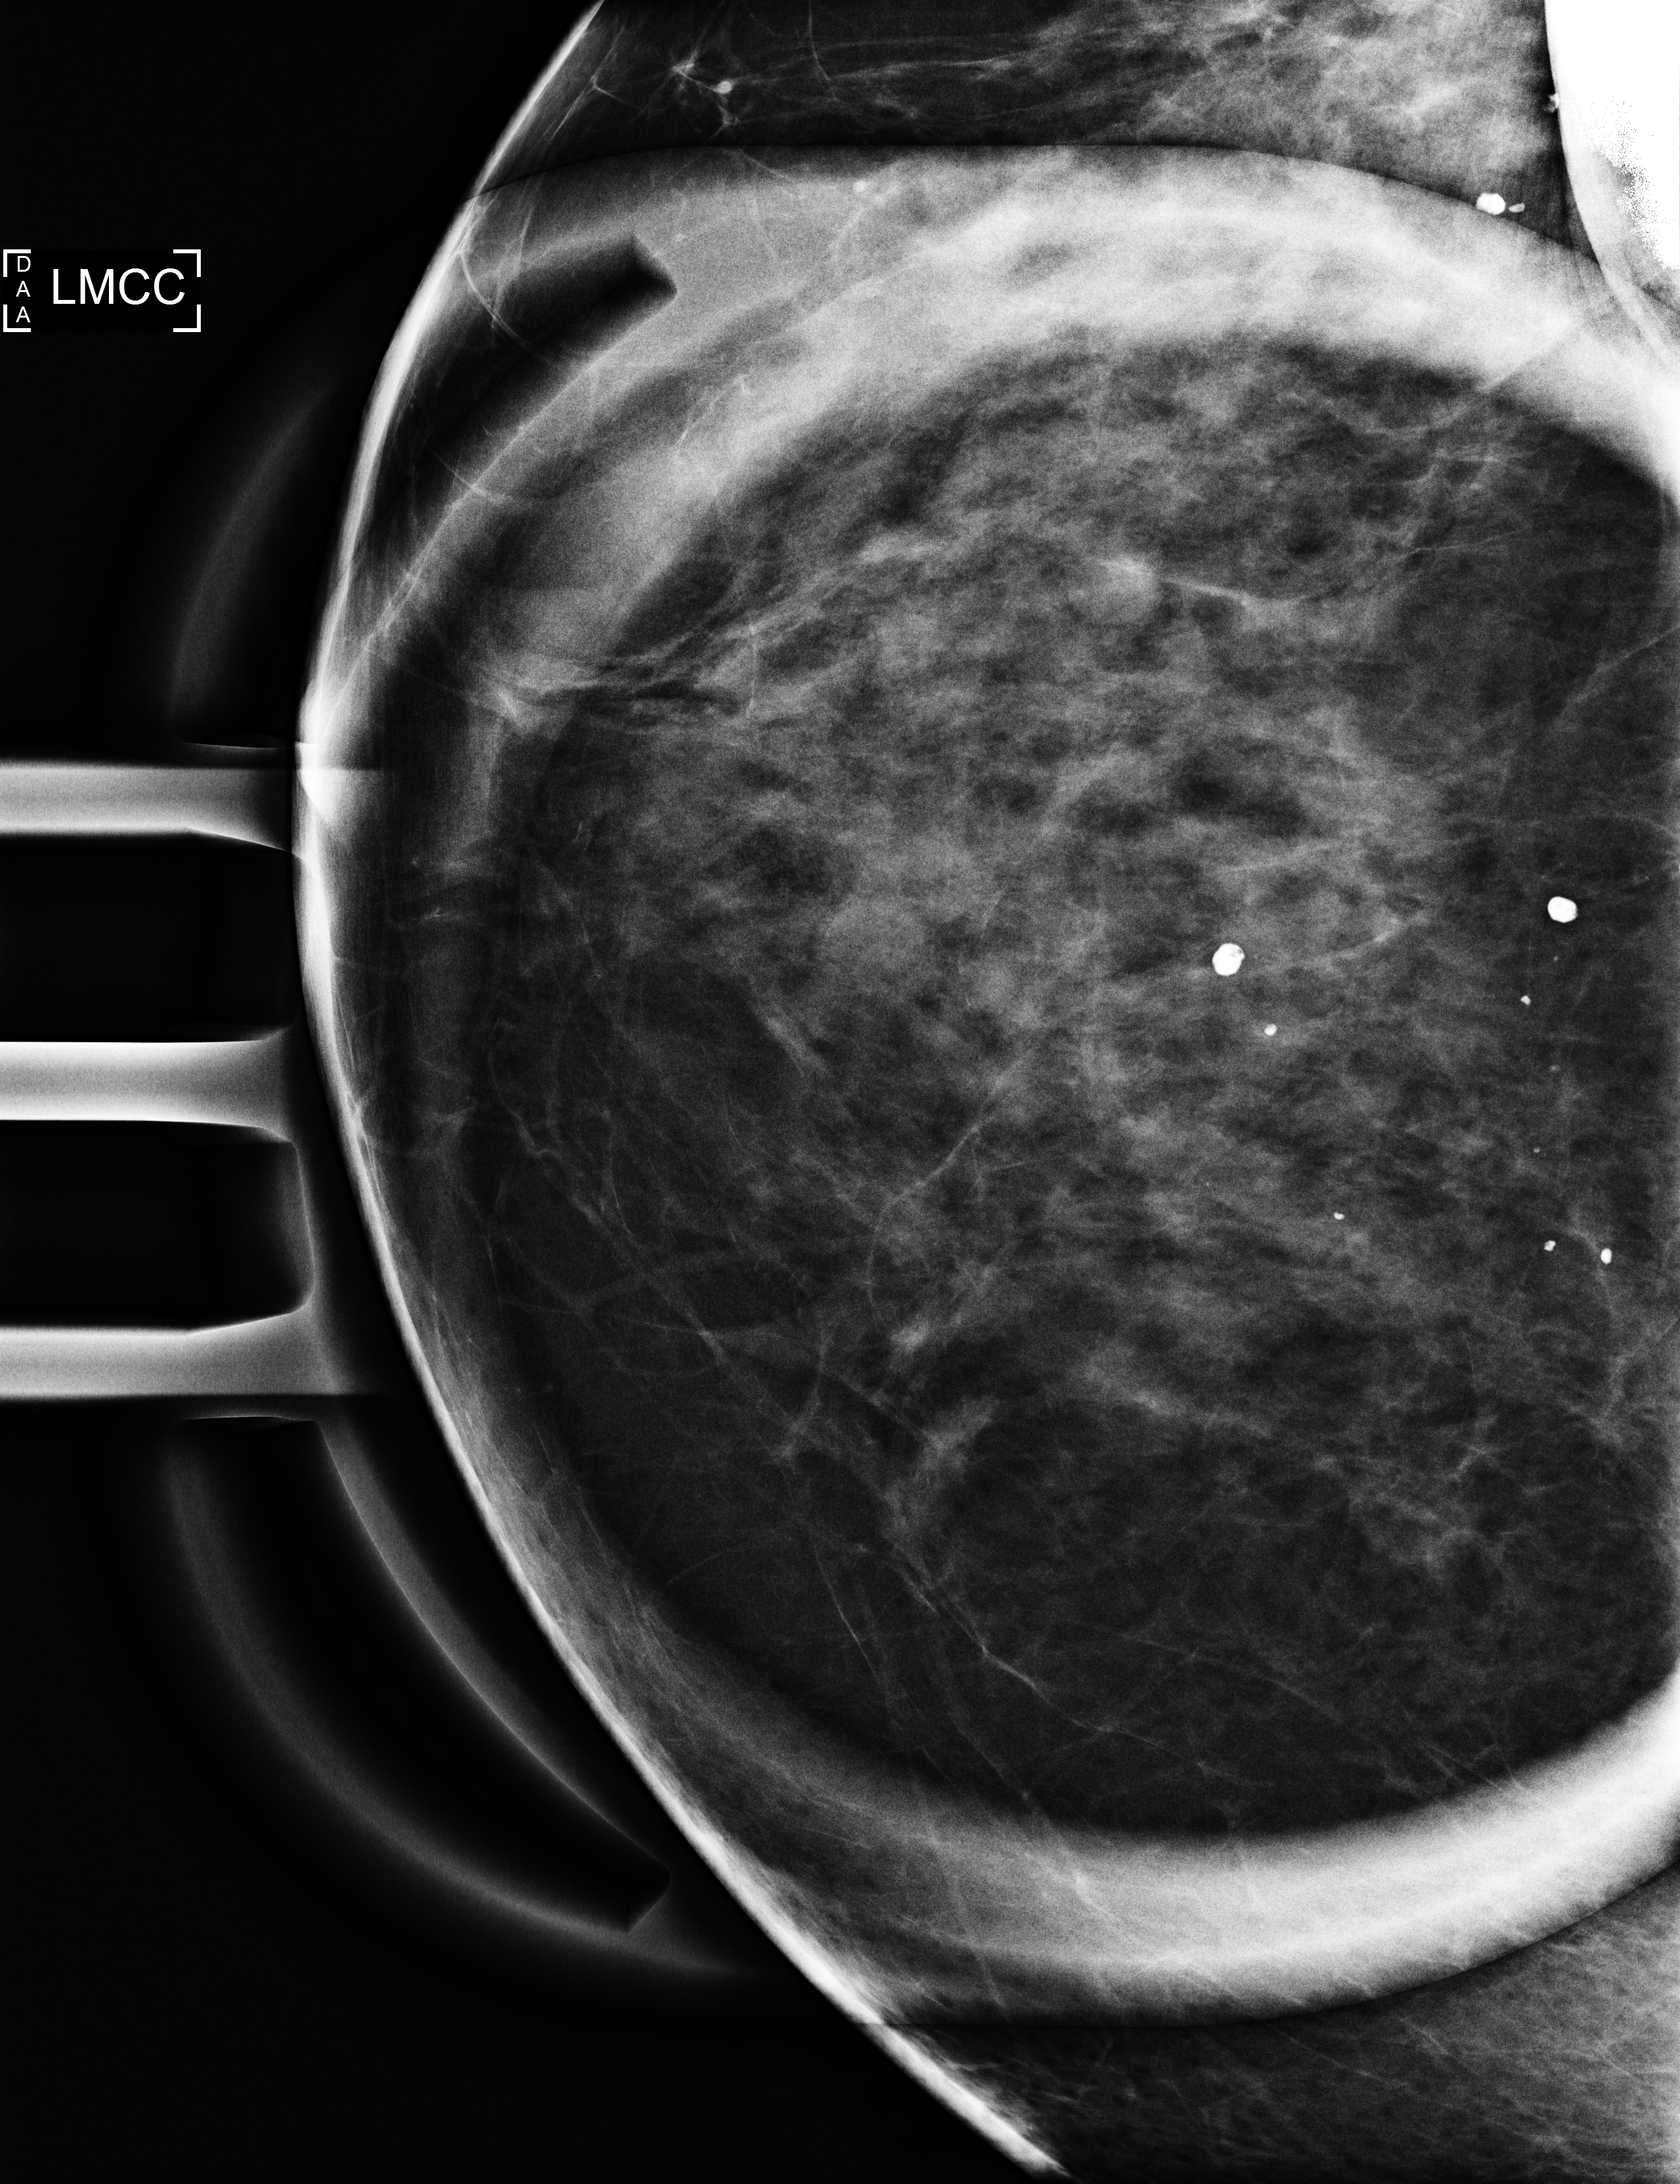
Digital mammogram (FFDM); left breast; cranio-caudal projection (magnification); additional (diagnostic) view; compressed breast thickness 50 mm; system: Selenia Dimensions. Patient aged 49 years (female).
Breast density at the screening exam (both breasts): heterogeneously dense (BI-RADS density category c). Final BI-RADS assessment for this screening round (tomosynthesis exam, both breasts): category 2. Recall: recalled for additional imaging after this screen.